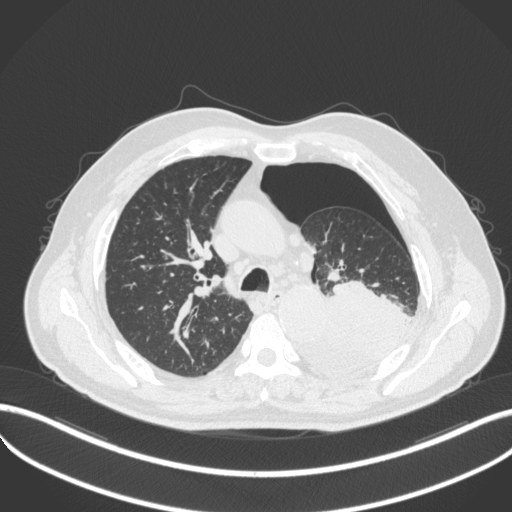
Chest CT, one axial slice; 120 kVp; lung window (W 1500 / L -600 HU); 1 mm slice thickness; 512 × 512 image matrix. Male patient, age 76 years. Case-level facts recorded for this patient, not image findings: clinical TNM (as recorded): T3 N0 M1b.
Structures marked on this image (rectangle marked by the reading radiologist):
- lung tumour (recorded histology: adenocarcinoma): box from (x=291, y=279) to (x=418, y=377) px